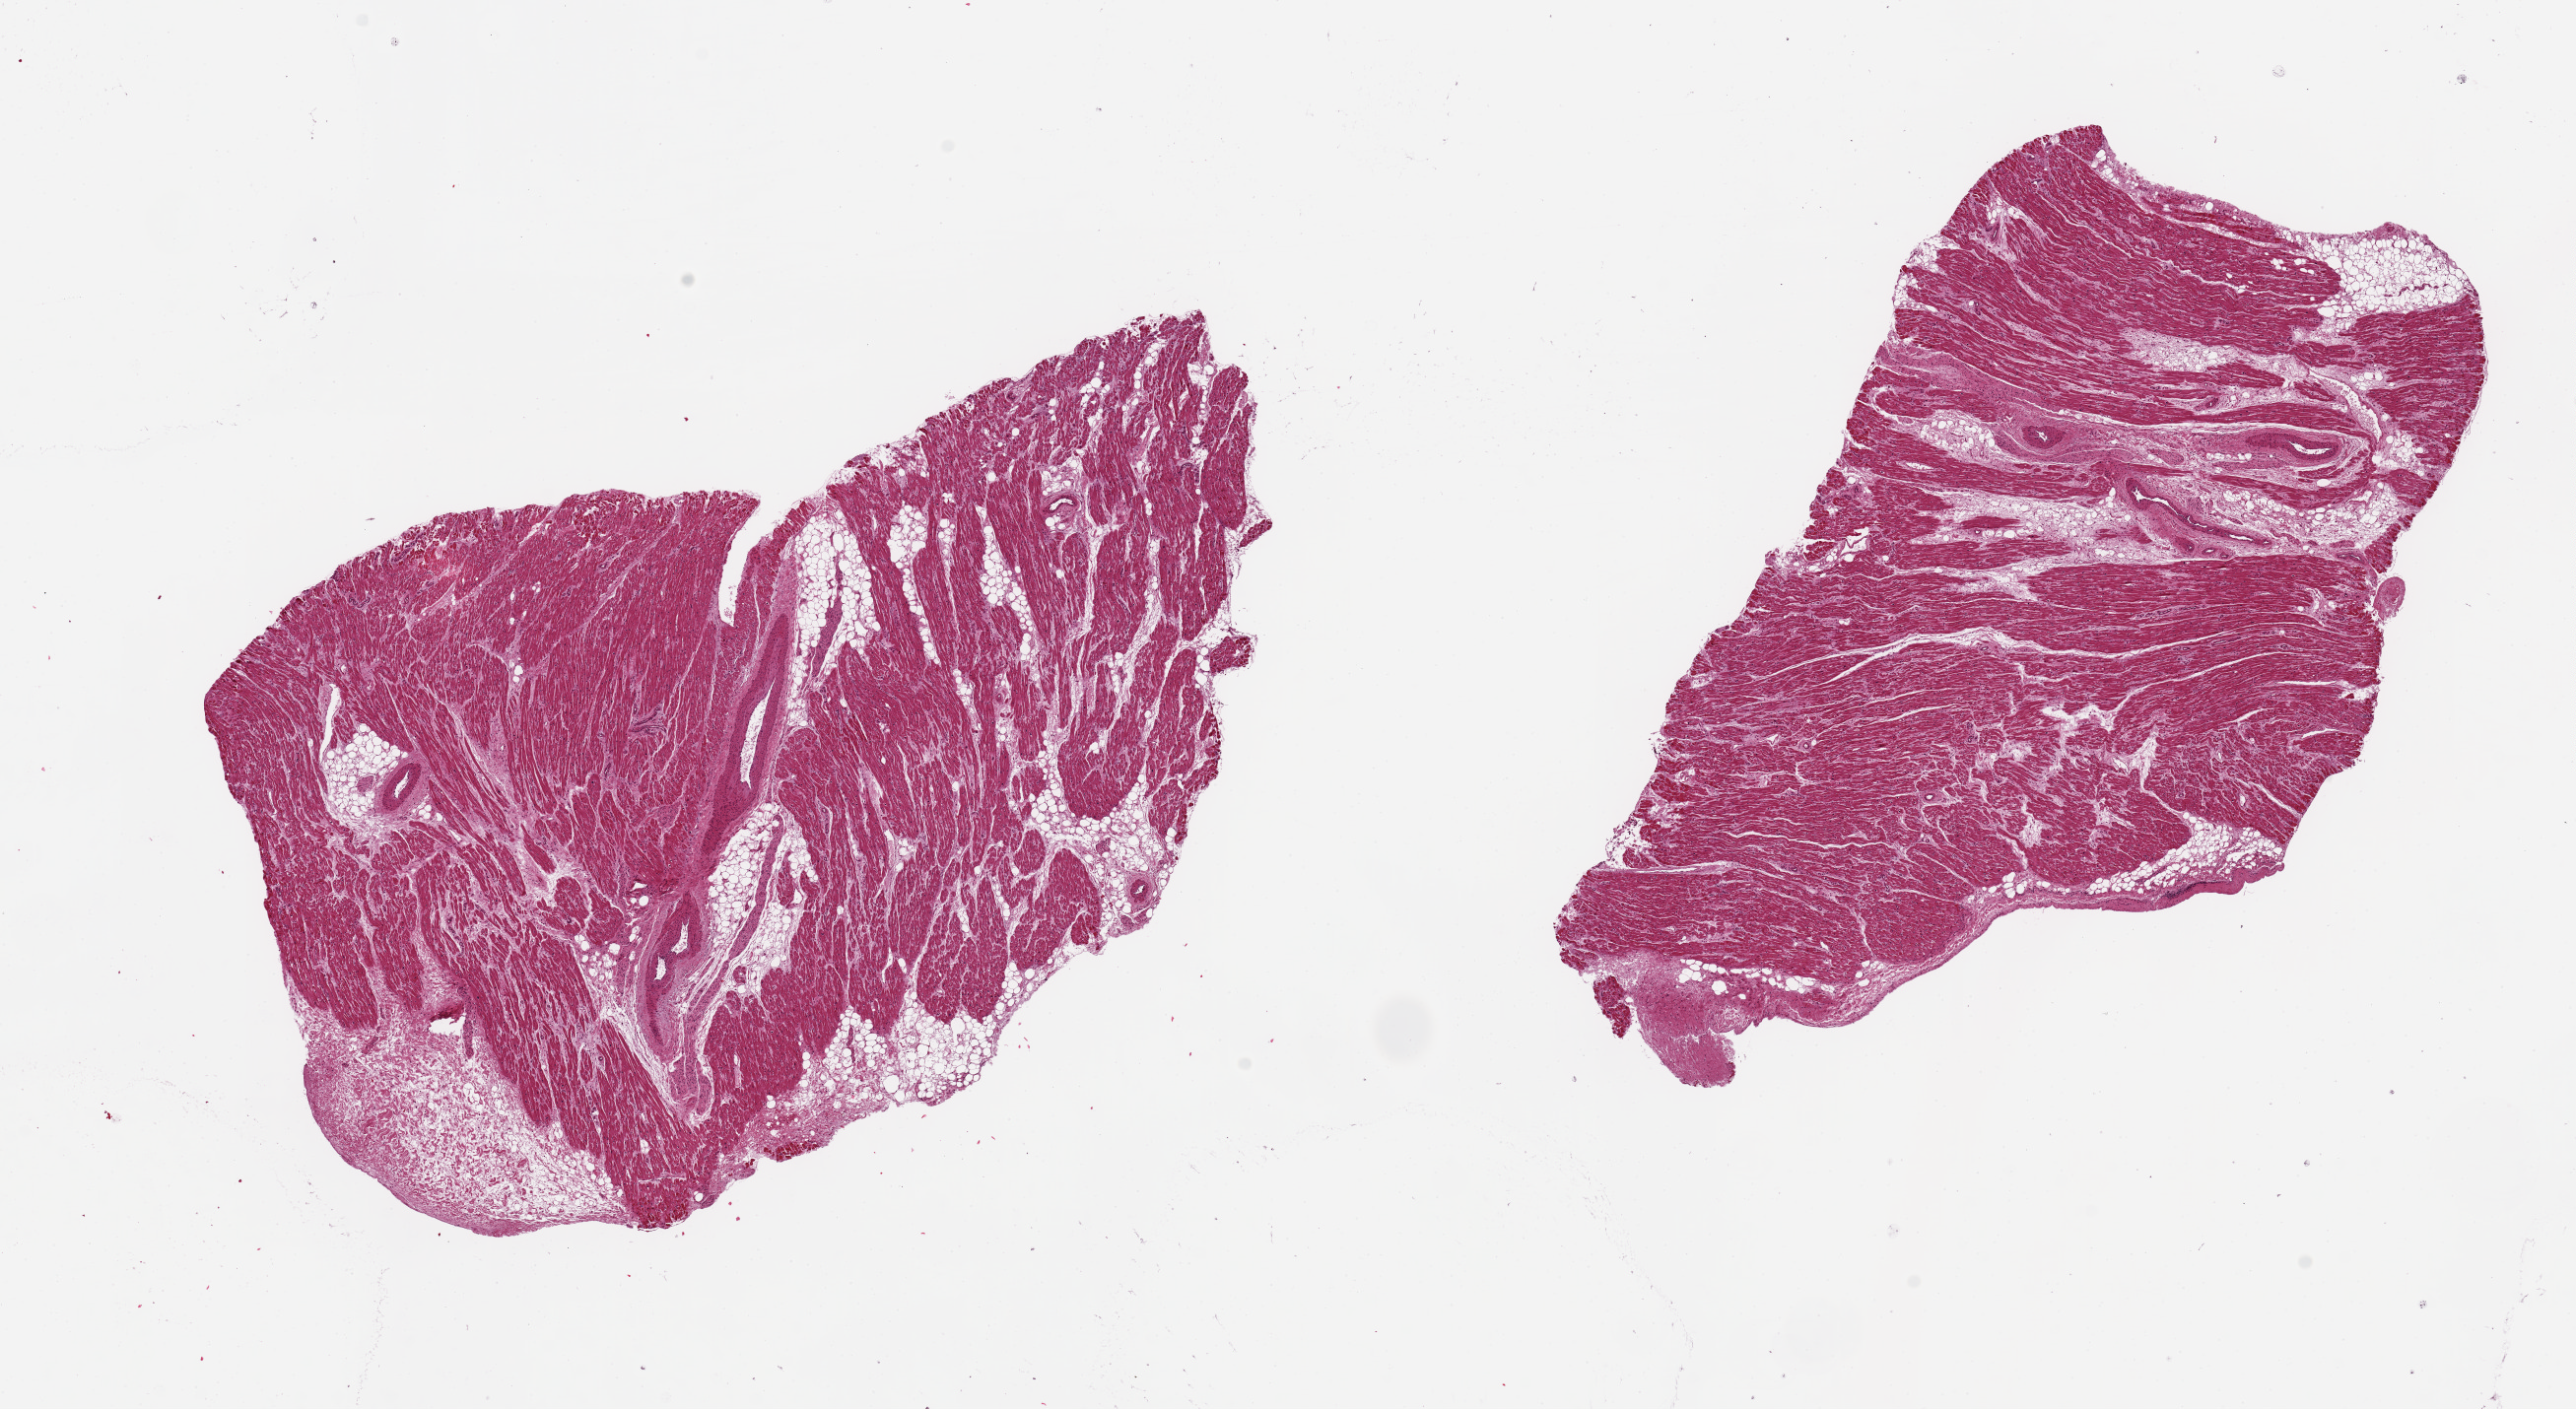
Haematoxylin and eosin whole-slide image, brightfield — whole scanned area (about 20.7 x 11.3 mm) shown as a low-resolution overview; PAXgene-fixed, paraffin-embedded tissue; target tissue: auricular appendage; tissue donor sample. Donor: male.
Review note (as recorded): 2 pieces, 9x6 & 8x5mm; hypertrophic fibers; 20% internal adipose.